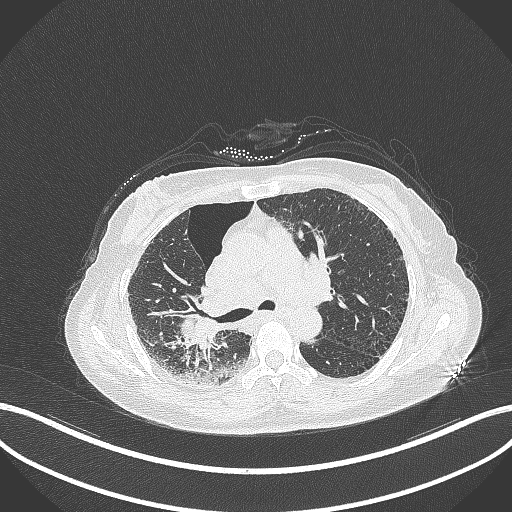
Chest CT, one axial slice. Reconstruction kernel B70f. Lung window (W 1500 / L -600 HU). 1 mm slice thickness. 512 × 512 image matrix, field of view 400 × 400 mm. Female patient, age 64 years. From the clinical record (not read from this slice): clinical TNM (as recorded): T3 N3 M0.
Outlined on this slice (rectangle marked by the reading radiologist):
- lung tumour (recorded histology: squamous cell carcinoma): box from (x=176, y=310) to (x=228, y=353) px